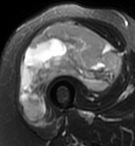
MRI of an extremity soft-tissue mass, one axial slice. Position 42 of 95 along the scan axis. T2-weighted fat-saturated. MR volume resampled by the dataset authors to the PET/CT grid (not the native acquisition matrix). 3.27 mm slice thickness. 135 × 146 image matrix, field of view 132 × 143 mm. Female patient. From the clinical record (not read from this slice): histological type: pleiomorphic undifferentiated sarcoma; grade: high; site of the primary tumour: right quadricep.
Annotated regions visible in this slice (expert contour drawn on MRI and transferred to this co-registered scan by the dataset authors):
- gross tumour volume including surrounding oedema: bounding box [x1, y1, x2, y2] px = [21, 22, 120, 119]
- gross tumour volume (mass): [21, 22, 120, 119]